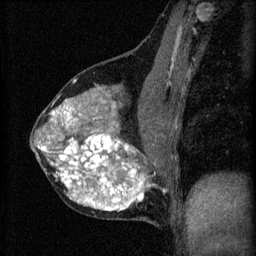
Breast MRI (dynamic contrast-enhanced), one sagittal slice. Position 31 of 60 along the scan axis. 3 images stored at this slice position (order not interpretable as contrast timing). 1.5 T. TE 4.2 ms, TR 8.2 ms. 2 mm slice thickness. 256 × 256 image matrix, field of view 180 × 180 mm. Female patient, age 40 years.
Structures marked on this image (semi-automatically segmented with operator editing):
- analysis volume of interest (the breast-tissue region the enhancement analysis was run in; not a lesion): bounding box [x1, y1, x2, y2] px = [30, 76, 179, 219]
- tumour enhancement mask (voxels above the 70 % enhancement threshold inside the analysis volume of interest): [38, 82, 147, 211]